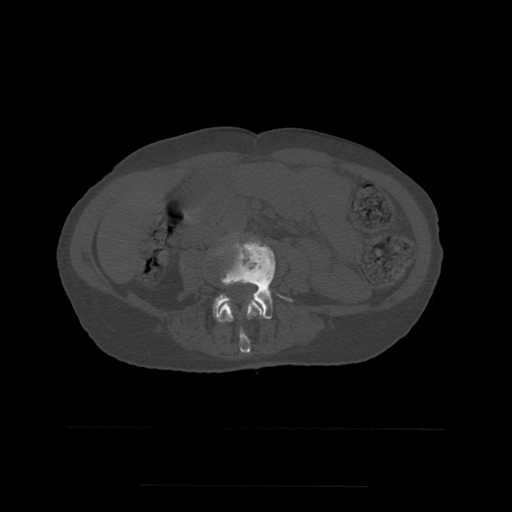
CT including the spine, one axial slice. Position 177 of 544 along the scan axis. Bone window (W 1800 / L 400 HU). 1.25 mm slice thickness. 512 × 512 image matrix. Patient age 58 years. From the clinical record (not read from this slice): primary cancer: lung.
Outlined on this slice (semi-automatically segmented with operator editing):
- L3 vertebra: bounding box (x1, y1, x2, y2) in pixels: (213, 245, 263, 354)
- L4 vertebra: (213, 240, 292, 321)